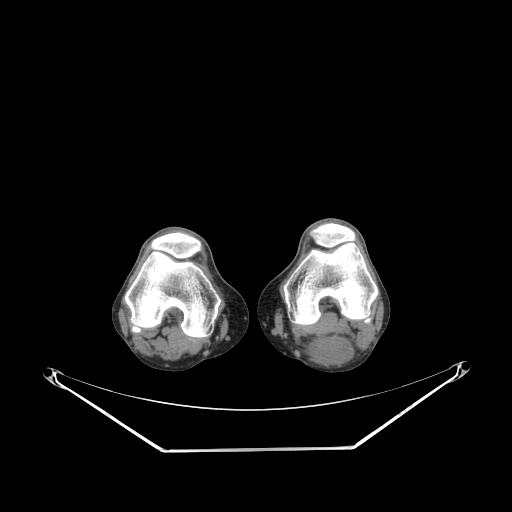
CT of an extremity soft-tissue mass (from a PET/CT study), one axial slice. Slice 177 of 267 in the series (ordered by position). Reconstruction kernel SOFT. Soft-tissue window (W 400 / L 40 HU). 3.75 mm slice thickness. 512 × 512 image matrix, field of view 500 × 500 mm. Male patient. From the clinical record (not read from this slice): histological type: synovial sarcoma; site of the primary tumour: left poplietal fossa.
Annotated regions visible in this slice (expert contour drawn on MRI and transferred to this co-registered scan by the dataset authors):
- gross tumour volume (mass): bounding box [x1, y1, x2, y2] px = [310, 333, 353, 364]